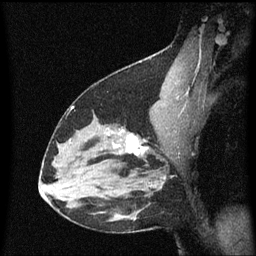
Breast MRI (dynamic contrast-enhanced), one sagittal slice; dynamic contrast-enhanced series, image 2 of 3 at this slice position (ordered by acquisition); 1.5 T; TE 4.2 ms, TR 8.4 ms; 2 mm slice thickness; 256 × 256 image matrix. Female patient, age 38 years. From the clinical record (not read from this slice): setting: breast cancer imaged before/during neoadjuvant chemotherapy; receptor status: HR-positive, HER2-negative.
Structures marked on this image (semi-automatic segmentation, software-assisted and operator-edited):
- analysis volume of interest (the breast-tissue region the enhancement analysis was run in; not a lesion): bounding box [x1, y1, x2, y2] px = [122, 128, 154, 163]
- tumour enhancement mask (voxels above the 70 % enhancement threshold inside the analysis volume of interest): [123, 130, 150, 155]